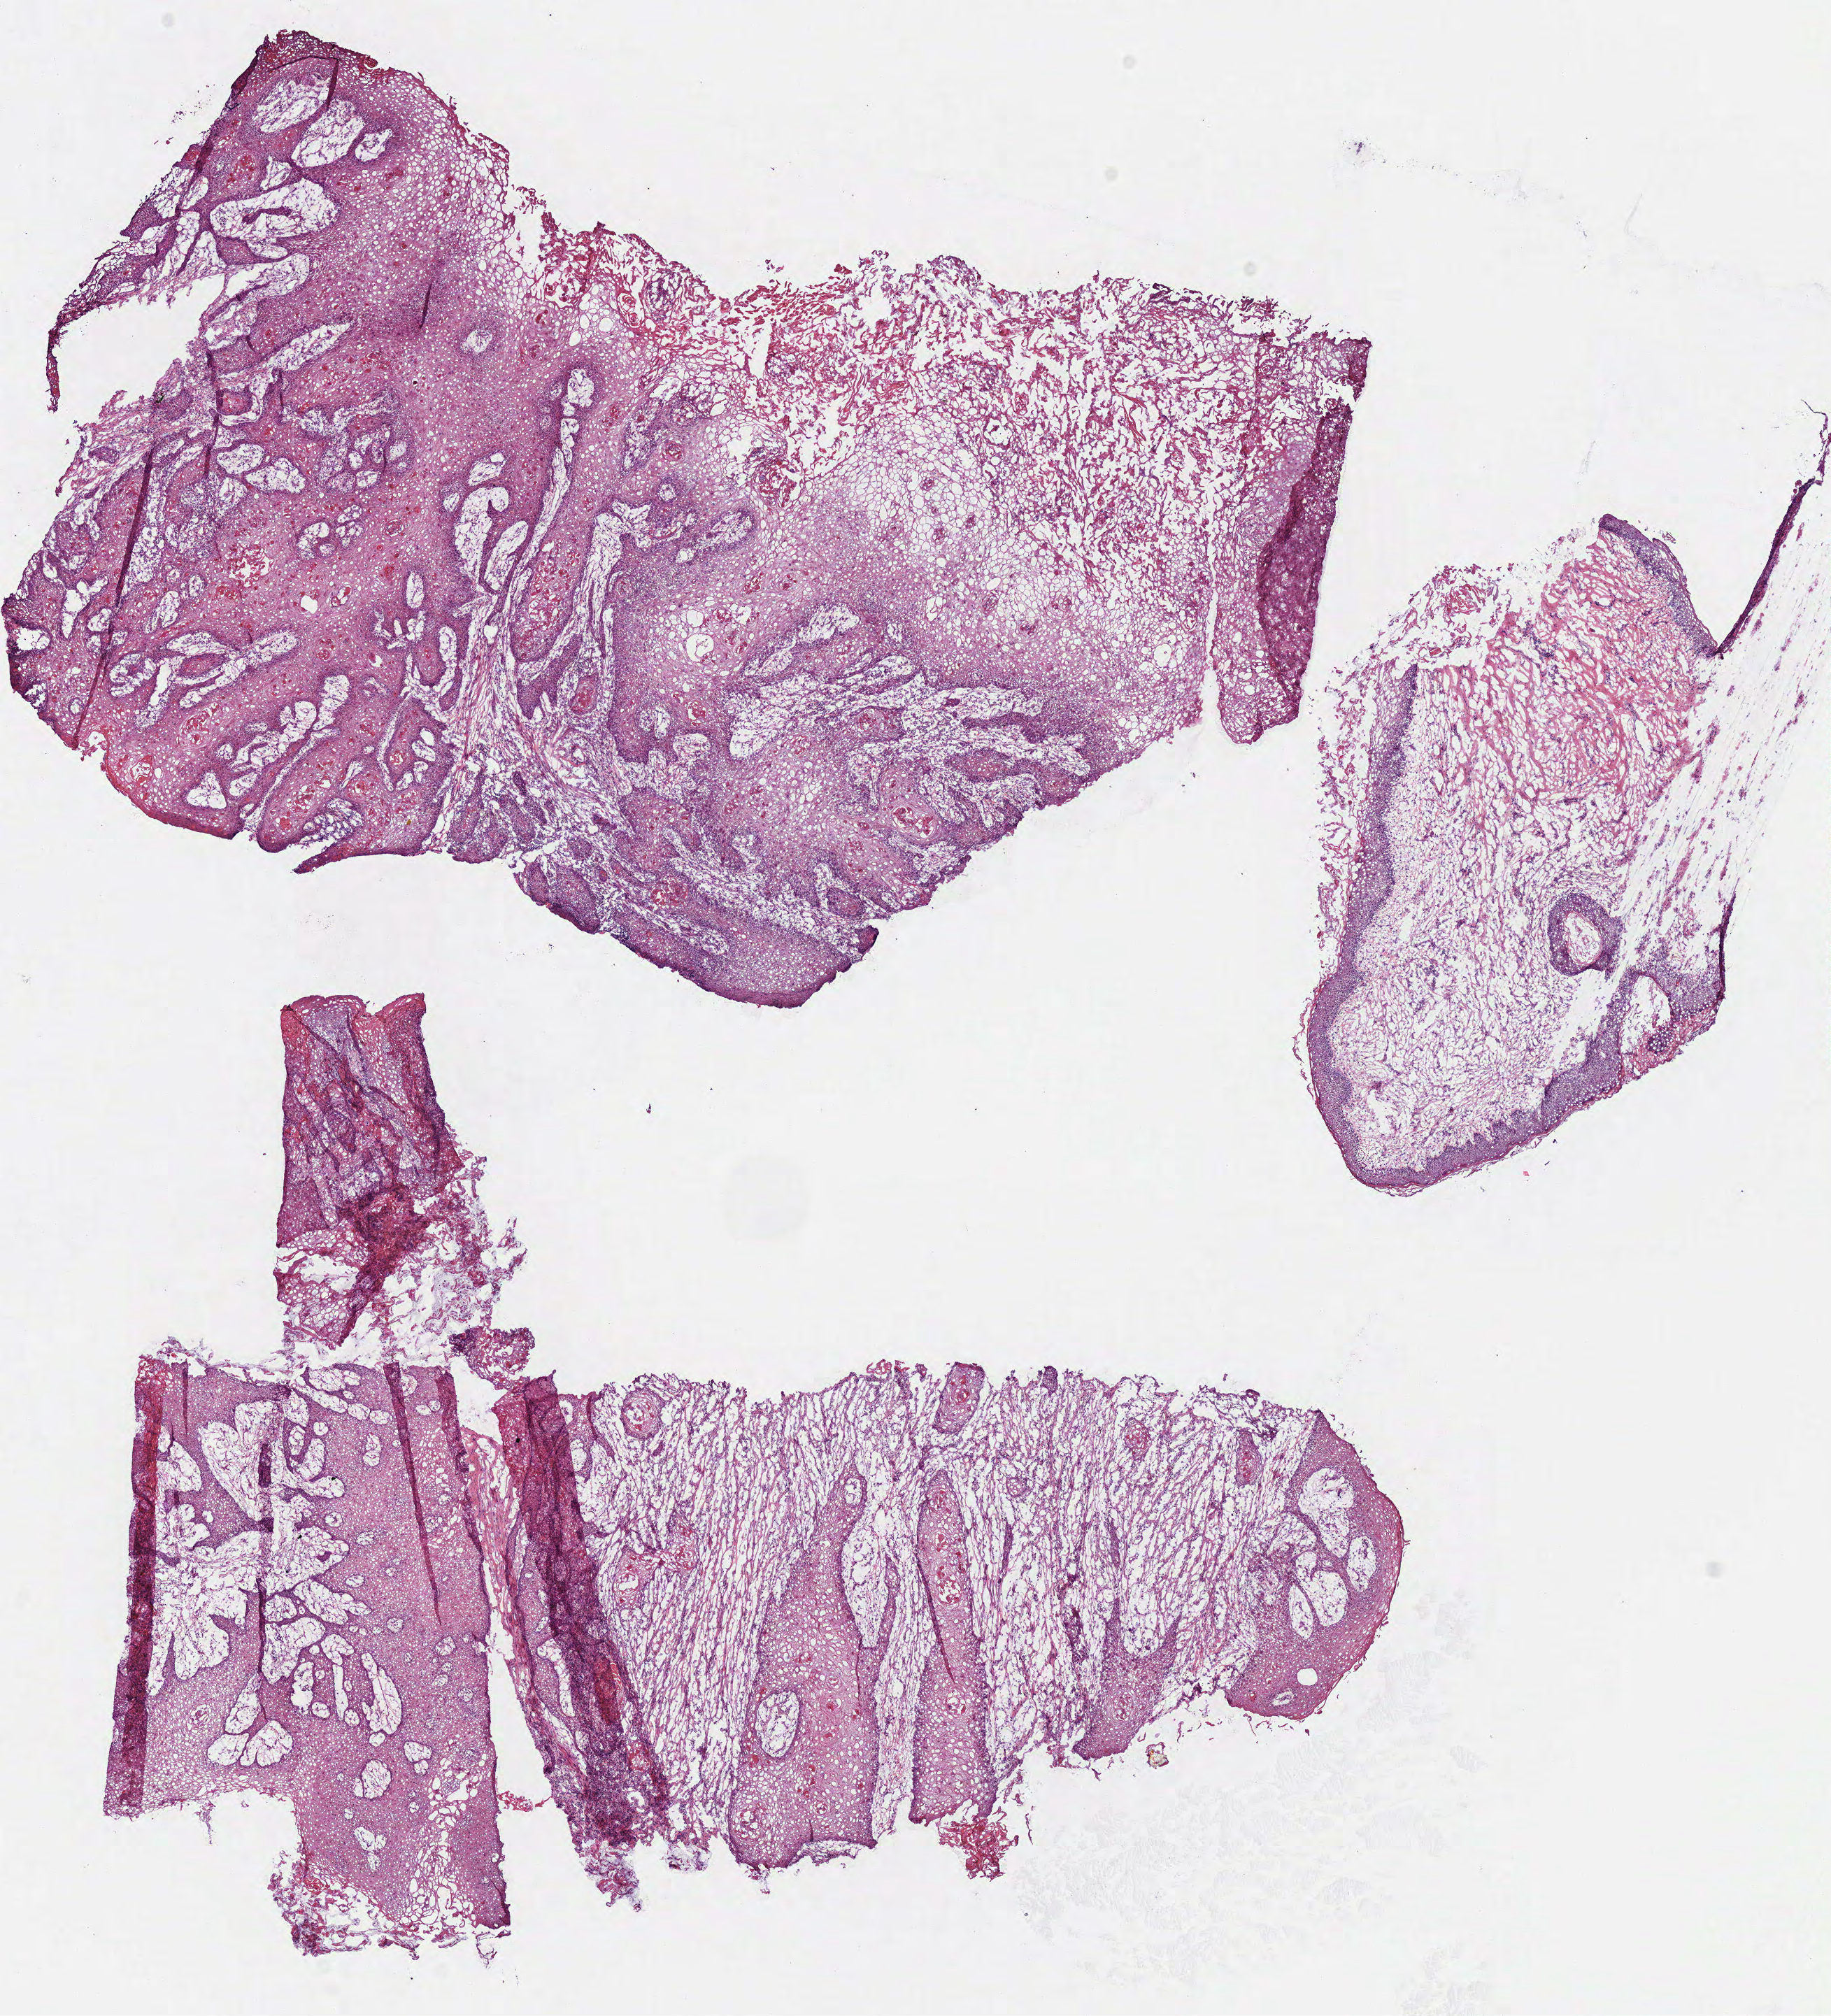
Hematoxylin and eosin (H&E) stained whole-slide image, shown as a low-resolution overview of the whole scanned area (about 10.3 x 11.4 mm), frozen section, head and neck, primary tumour sample. Male, age 52 years at initial diagnosis. Histologic grade: G1 (well differentiated). Composition of this section per pathologist review: tumour cells 70%, tumour nuclei 80%, normal cells 0%, stromal cells 30%, necrosis 0%. Infiltration values recorded for this section: lymphocyte infiltration 9%, monocyte infiltration 0%, neutrophil infiltration 0%.
AJCC pathologic stage: II (7th edition). TNM: T2 N0. Pathologic diagnosis: Squamous cell carcinoma, NOS (overlapping lesion of lip, oral cavity and pharynx).